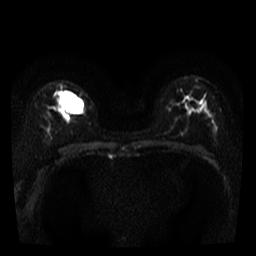
Breast MRI, one axial slice. Slice 23 of 40 in the series (ordered by position). Diffusion-weighted series; image 2 of 4 stored at this slice position (different b-values; order by instance number). 3 T. 256 × 256 image matrix, field of view 280 × 280 mm. Female patient.
Outlined on this slice (outlined manually by an expert reader):
- tumour on diffusion-weighted imaging: bounding box [x1, y1, x2, y2] px = [61, 91, 81, 112]